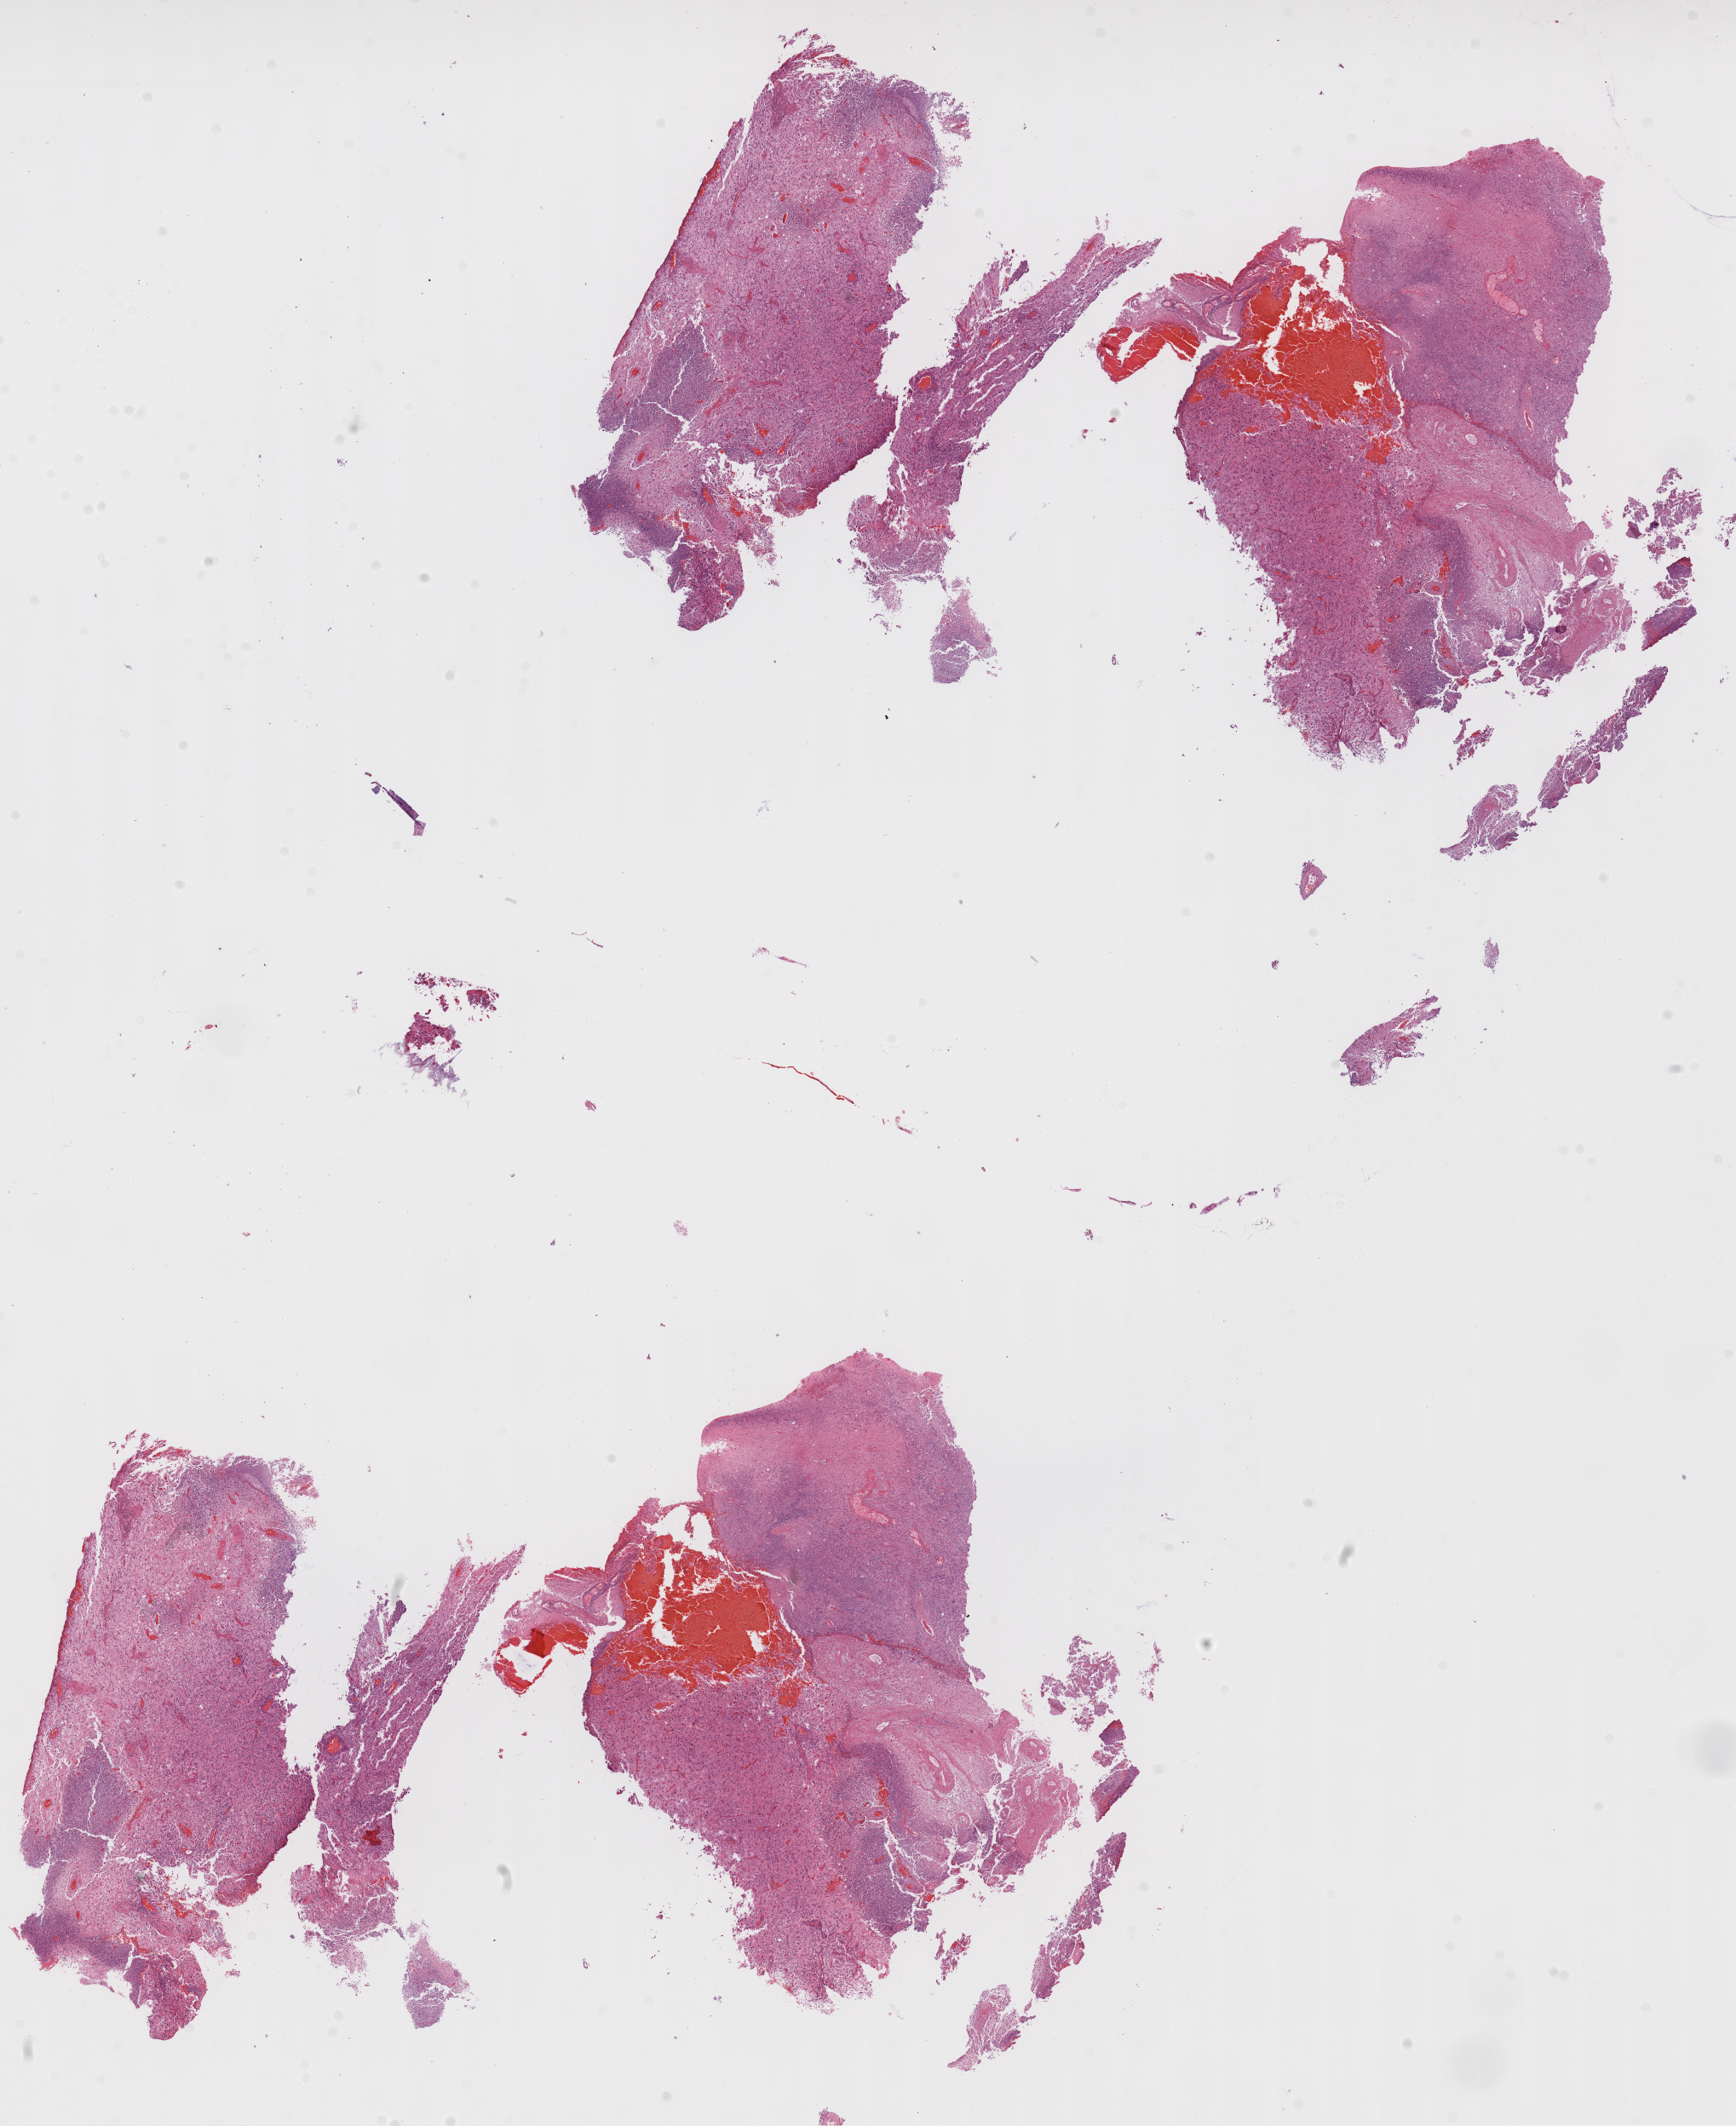
Digitized H&E-stained tissue section (whole slide) — whole scanned area (about 16.4 x 20.1 mm, from a 20x scan) shown as a low-resolution overview, formalin-fixed paraffin-embedded (FFPE) diagnostic section, sample: primary tumour, brain. Patient: male, age at initial diagnosis 62 years.
Diagnosis: Glioblastoma.